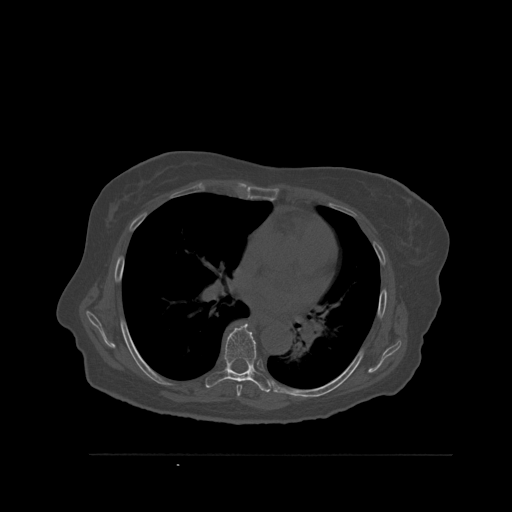
CT including the spine, one axial slice; slice 368 of 527 in the series (ordered by position); bone window (W 1800 / L 400 HU); 512 × 512 image matrix, field of view 470 × 470 mm. Female patient, age 73 years. From the clinical record (not read from this slice): primary cancer: breast.
Outlined on this slice (semi-automatic segmentation, software-assisted and operator-edited):
- T6 vertebra: bounding box <236,385,242,397> (left, top, right, bottom; pixels)
- T7 vertebra: <205,323,272,393>